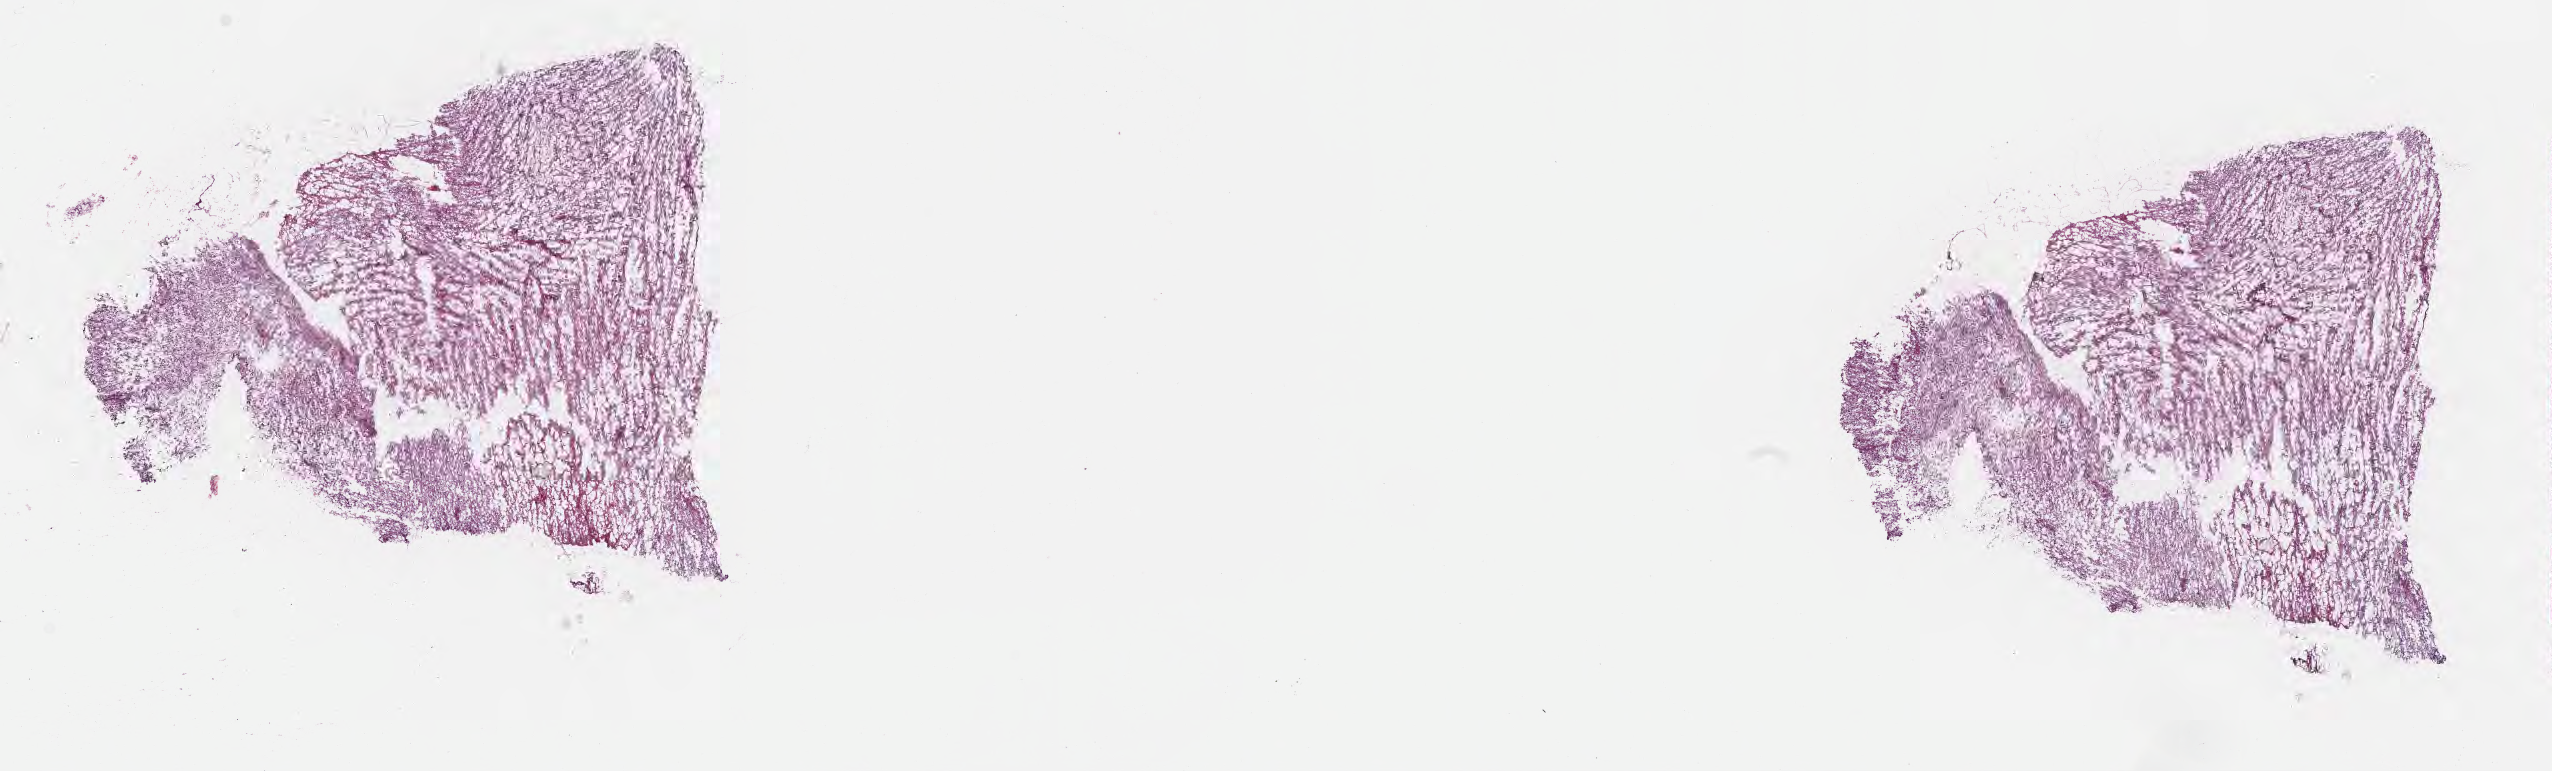
Digitized hematoxylin and eosin (H&E)-stained section — shown as a low-resolution overview of the whole scanned area (about 20.6 x 6.2 mm); frozen section (tissue freezing medium); primary tumor; anatomic site: brain. Male, age 75 years at initial diagnosis. Composition of this section per pathologist review: tumor cells 83%, tumor nuclei 92%, stromal cells 5%, necrosis 5%, normal cells 7%. Inflammatory infiltration, as recorded: lymphocyte infiltration 0%, monocyte infiltration 0%, neutrophil infiltration 0%.
- diagnosis: Glioblastoma, NOS
- section: top of the tissue portion